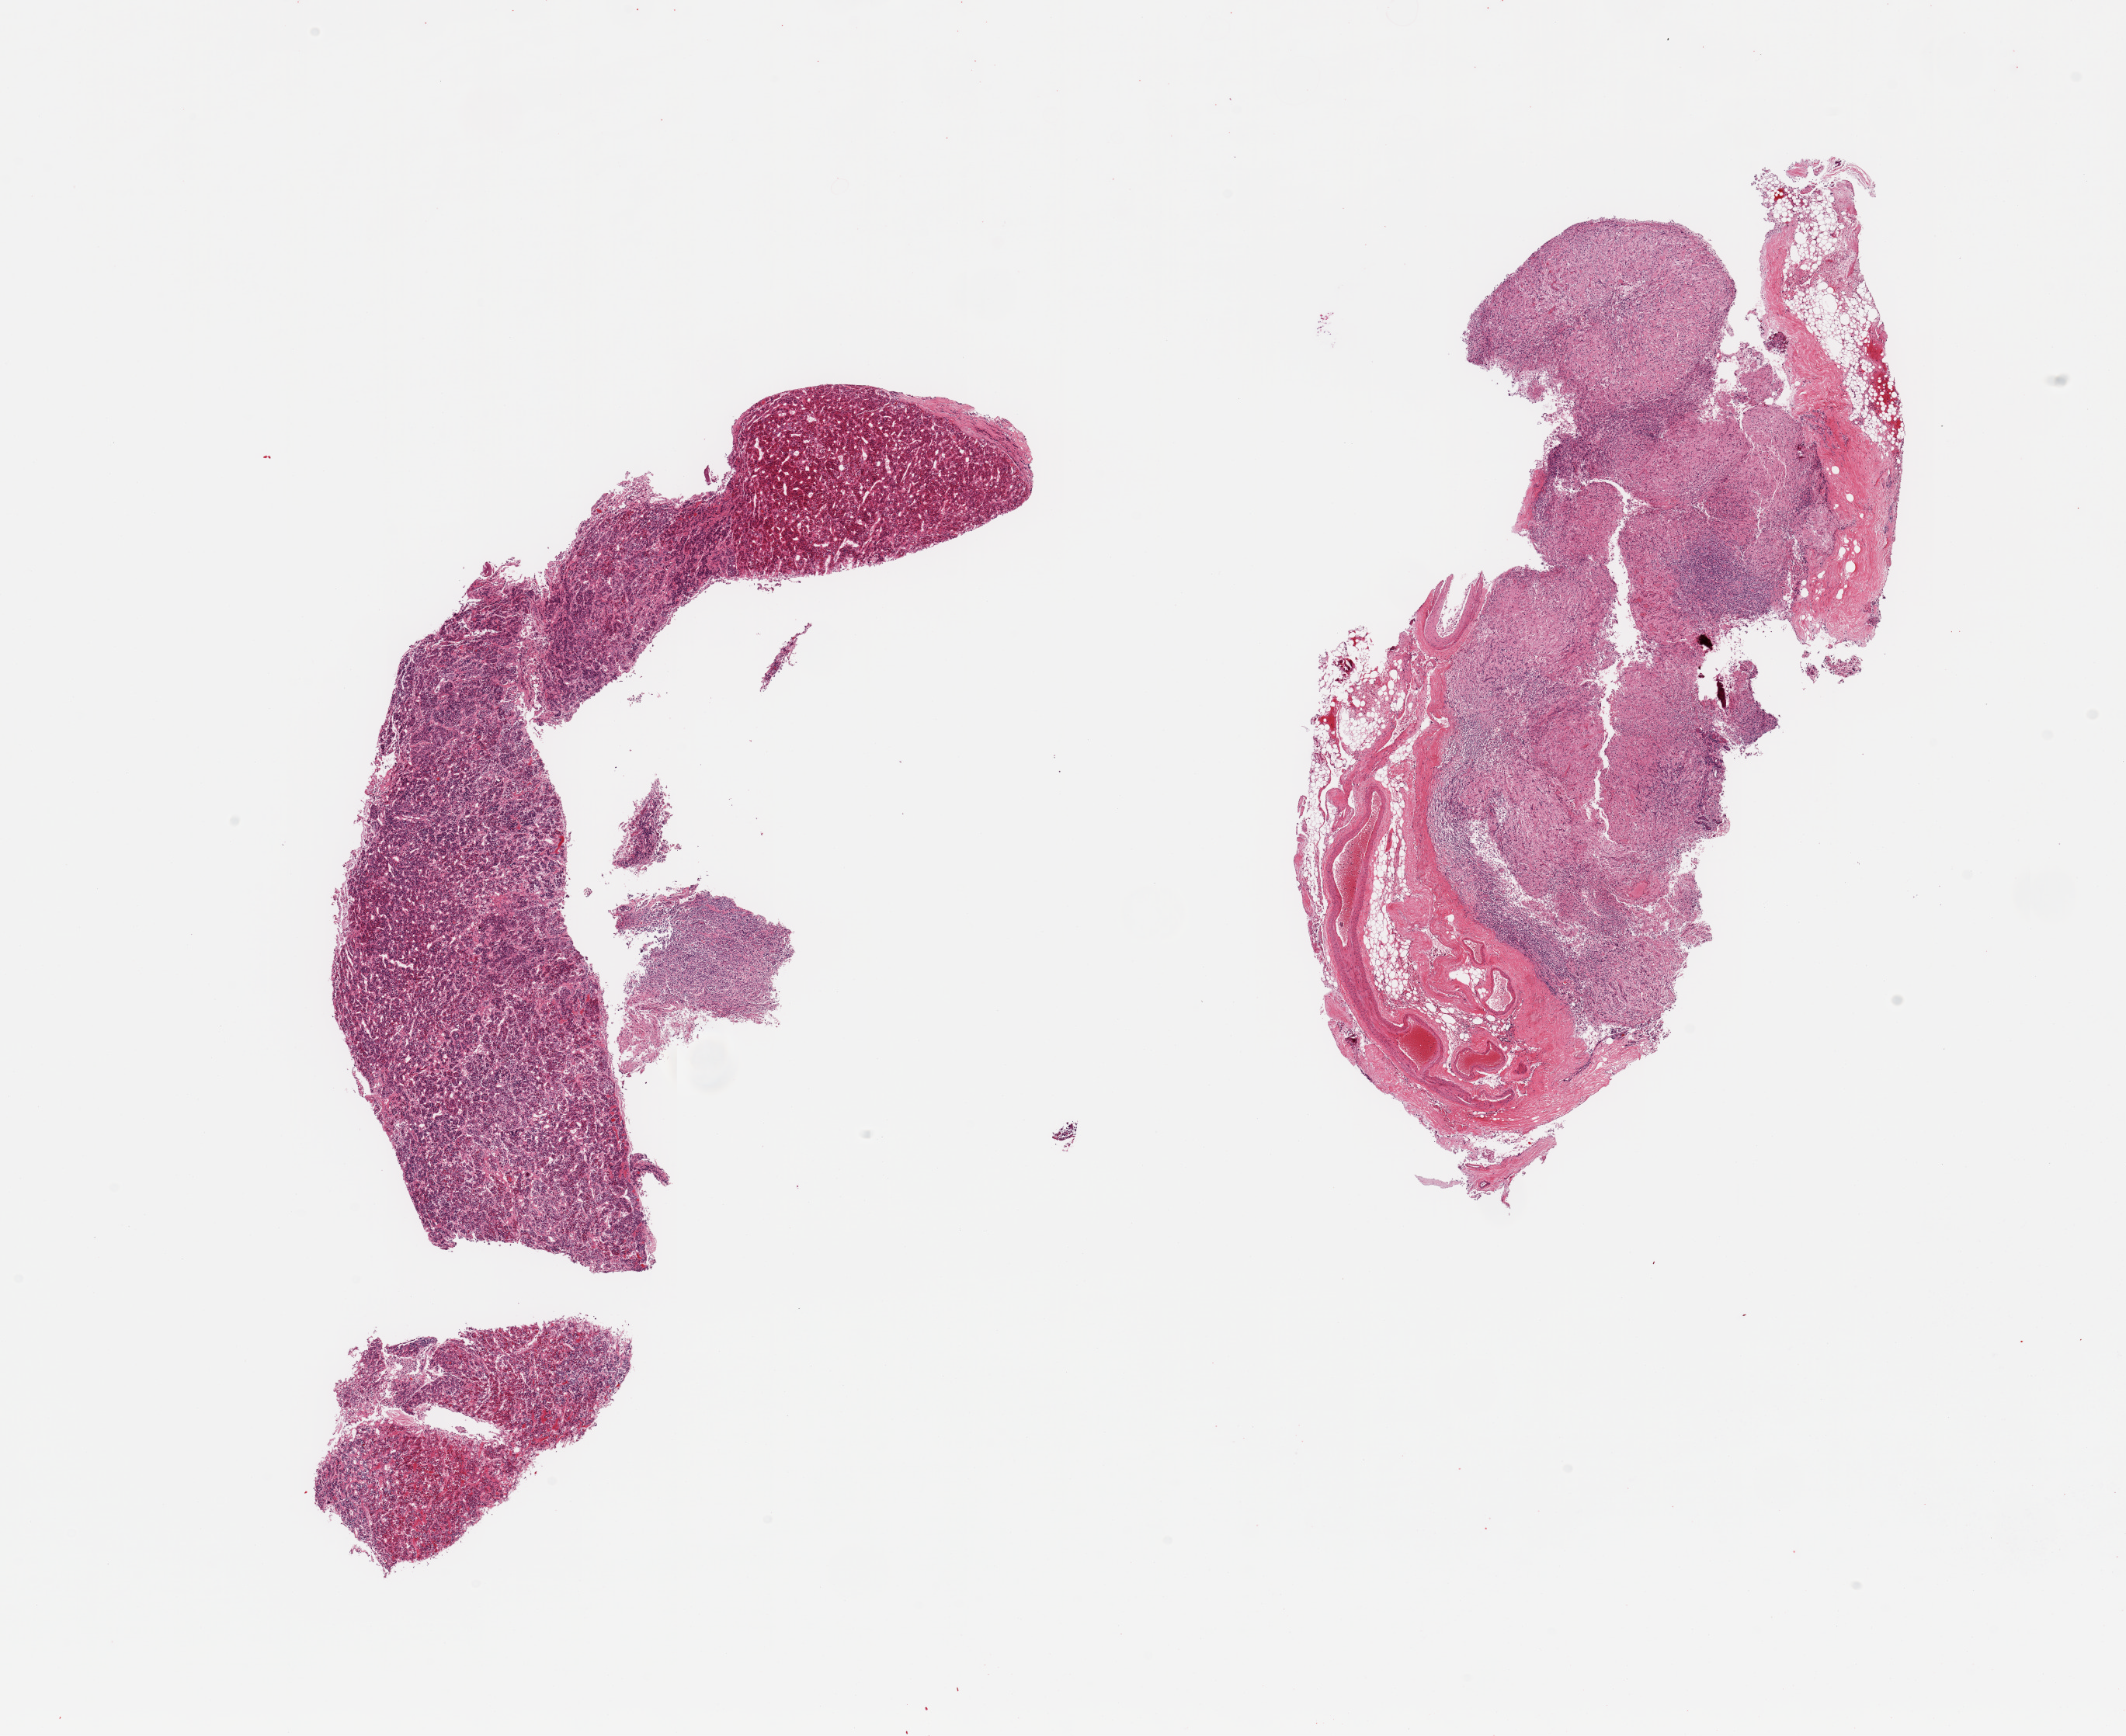
H&E whole-slide image, a low-resolution overview of the entire scanned area, about 21.7 x 17.7 mm (acquisition: 20x scan). PAXgene-fixed paraffin-embedded (PFPE) section. Section of pituitary (target tissue). Tissue donor sample. Donor: male.
• reviewer comment on this tissue sample: 2 pieces, no abnormalities ~50% neurohypophysis; adenohypophysis; rest is dura/connective tissue